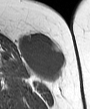
MRI of an extremity soft-tissue mass, one axial slice. Slice 19 of 45 in the series (ordered by position). MR volume resampled by the dataset authors to the PET/CT grid (not the native acquisition matrix). 3.27 mm slice thickness. 90 × 109 image matrix, field of view 88 × 106 mm. Female patient. From the clinical record (not read from this slice): histological type: leiomyosarcoma; grade: intermediate; site of the primary tumour: parascapusular.
Outlined on this slice (expert contour drawn on MRI and transferred to this co-registered scan by the dataset authors):
- gross tumour volume including surrounding oedema: bounding box <19,32,66,81> (left, top, right, bottom; pixels)
- gross tumour volume (mass): <19,32,66,81>